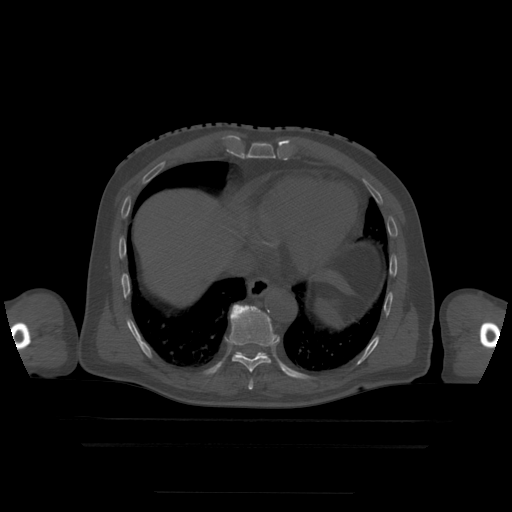
CT including the spine, one axial slice; position 258 of 522 along the scan axis; bone window (W 1800 / L 400 HU); 1.25 mm slice thickness; 512 × 512 image matrix, field of view 436 × 436 mm. Patient age 68 years. Case-level facts recorded for this patient, not image findings: primary cancer: urothelial.
Annotated regions visible in this slice (semi-automatic segmentation, software-assisted and operator-edited):
- T10 vertebra: bounding box (x1, y1, x2, y2) in pixels: (236, 352, 267, 357)
- T8 vertebra: (249, 380, 254, 390)
- T9 vertebra: (229, 305, 277, 373)